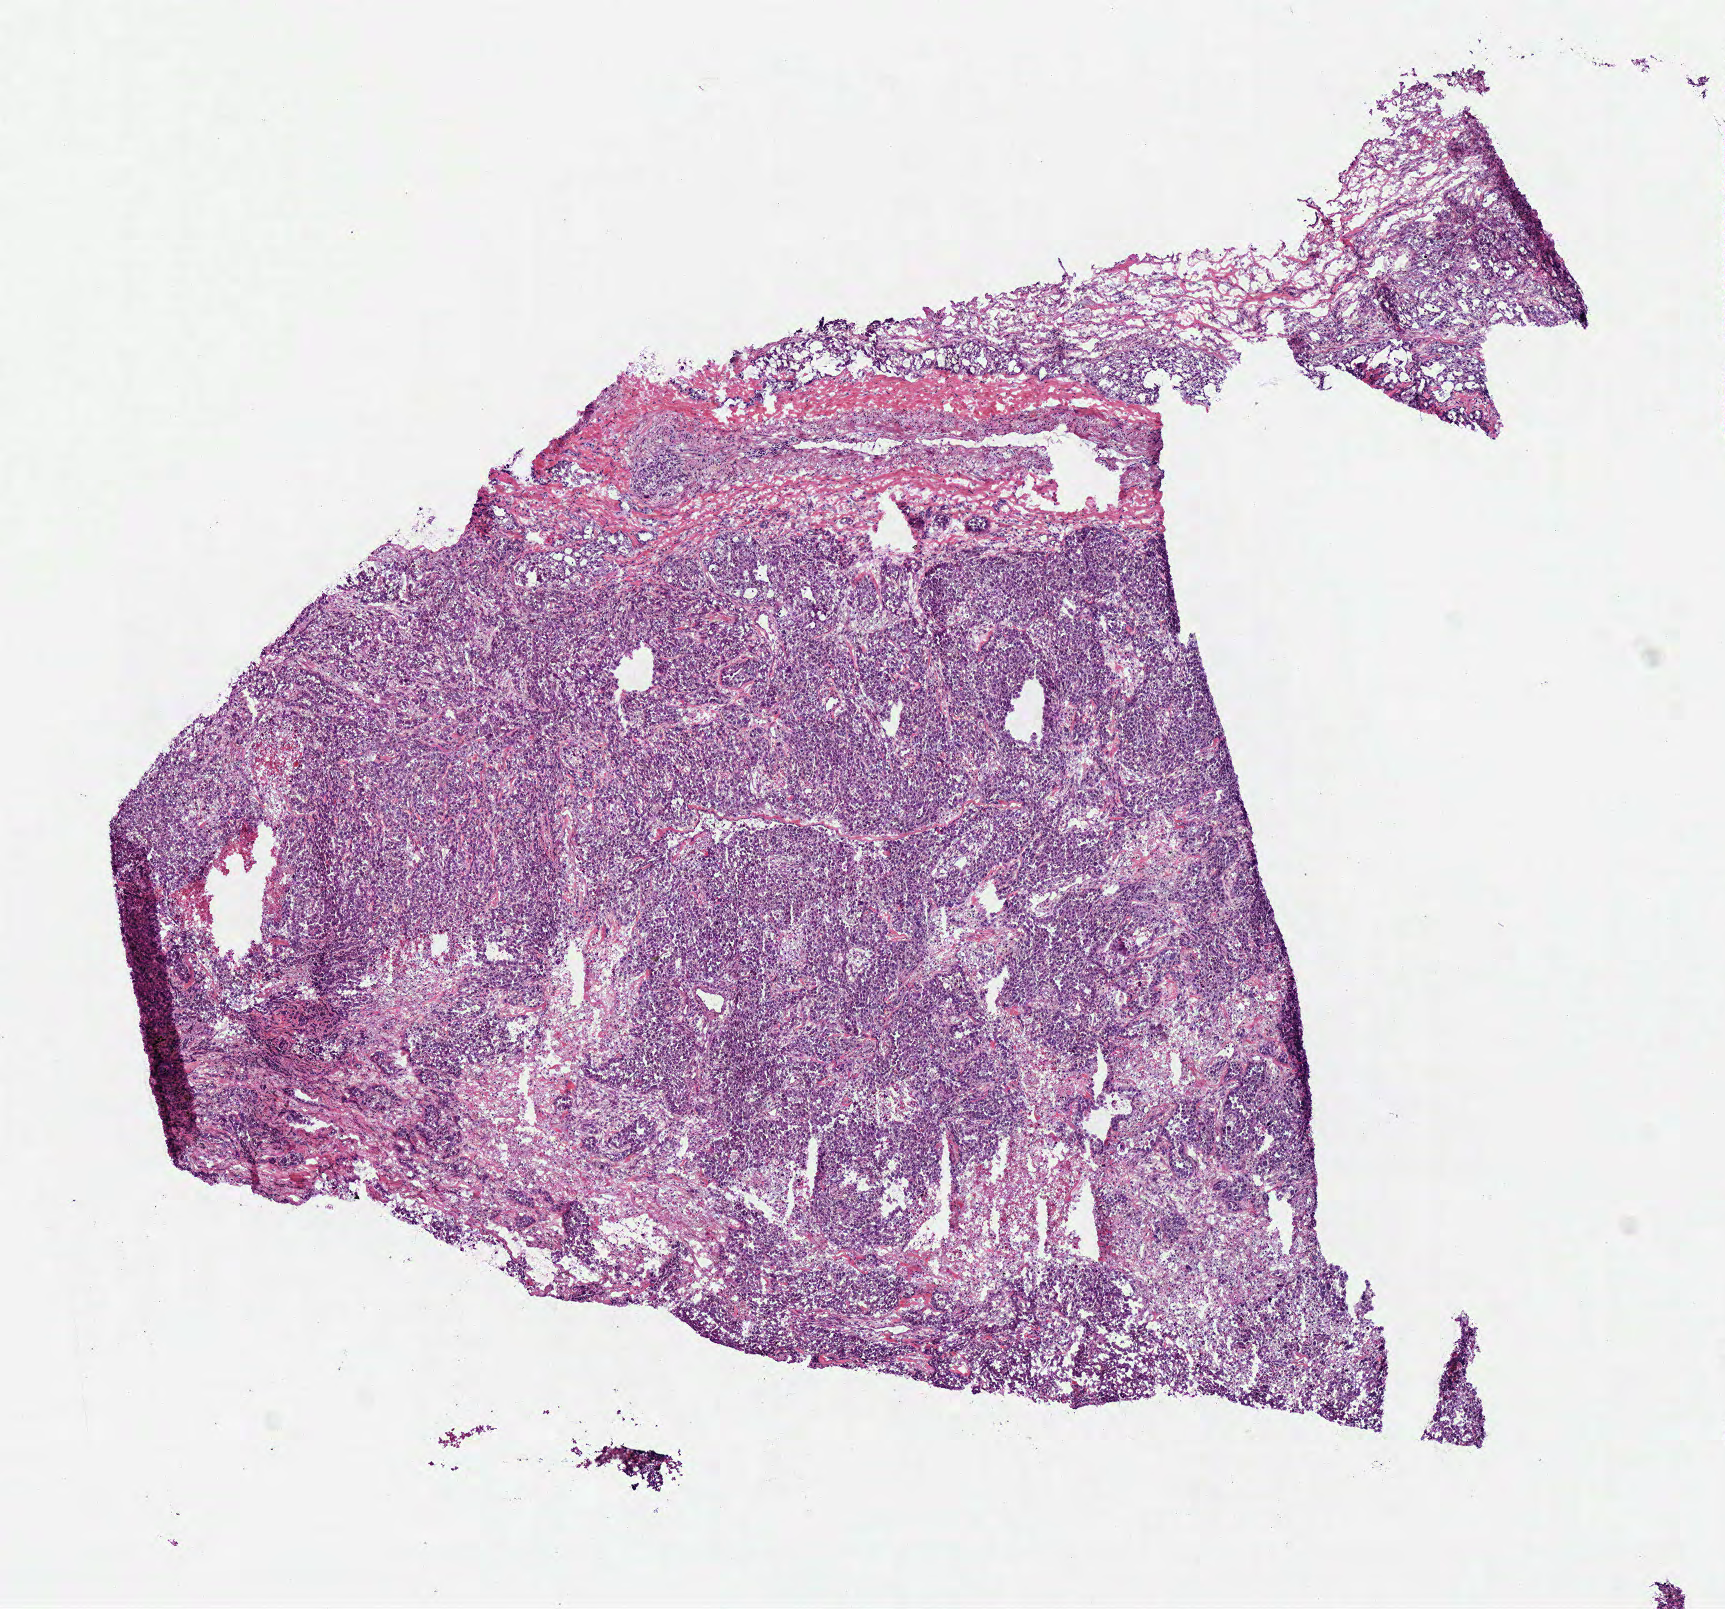
Whole-slide histology image, Hematoxylin and eosin (H&E) stained — a low-resolution overview of the entire scanned area, about 6.8 x 6.3 mm (slide scanned at 40x), frozen section from the bottom of the tissue portion, primary tumour sample from the lung. Patient sex: male.
Diagnosis: Adenocarcinoma, NOS.